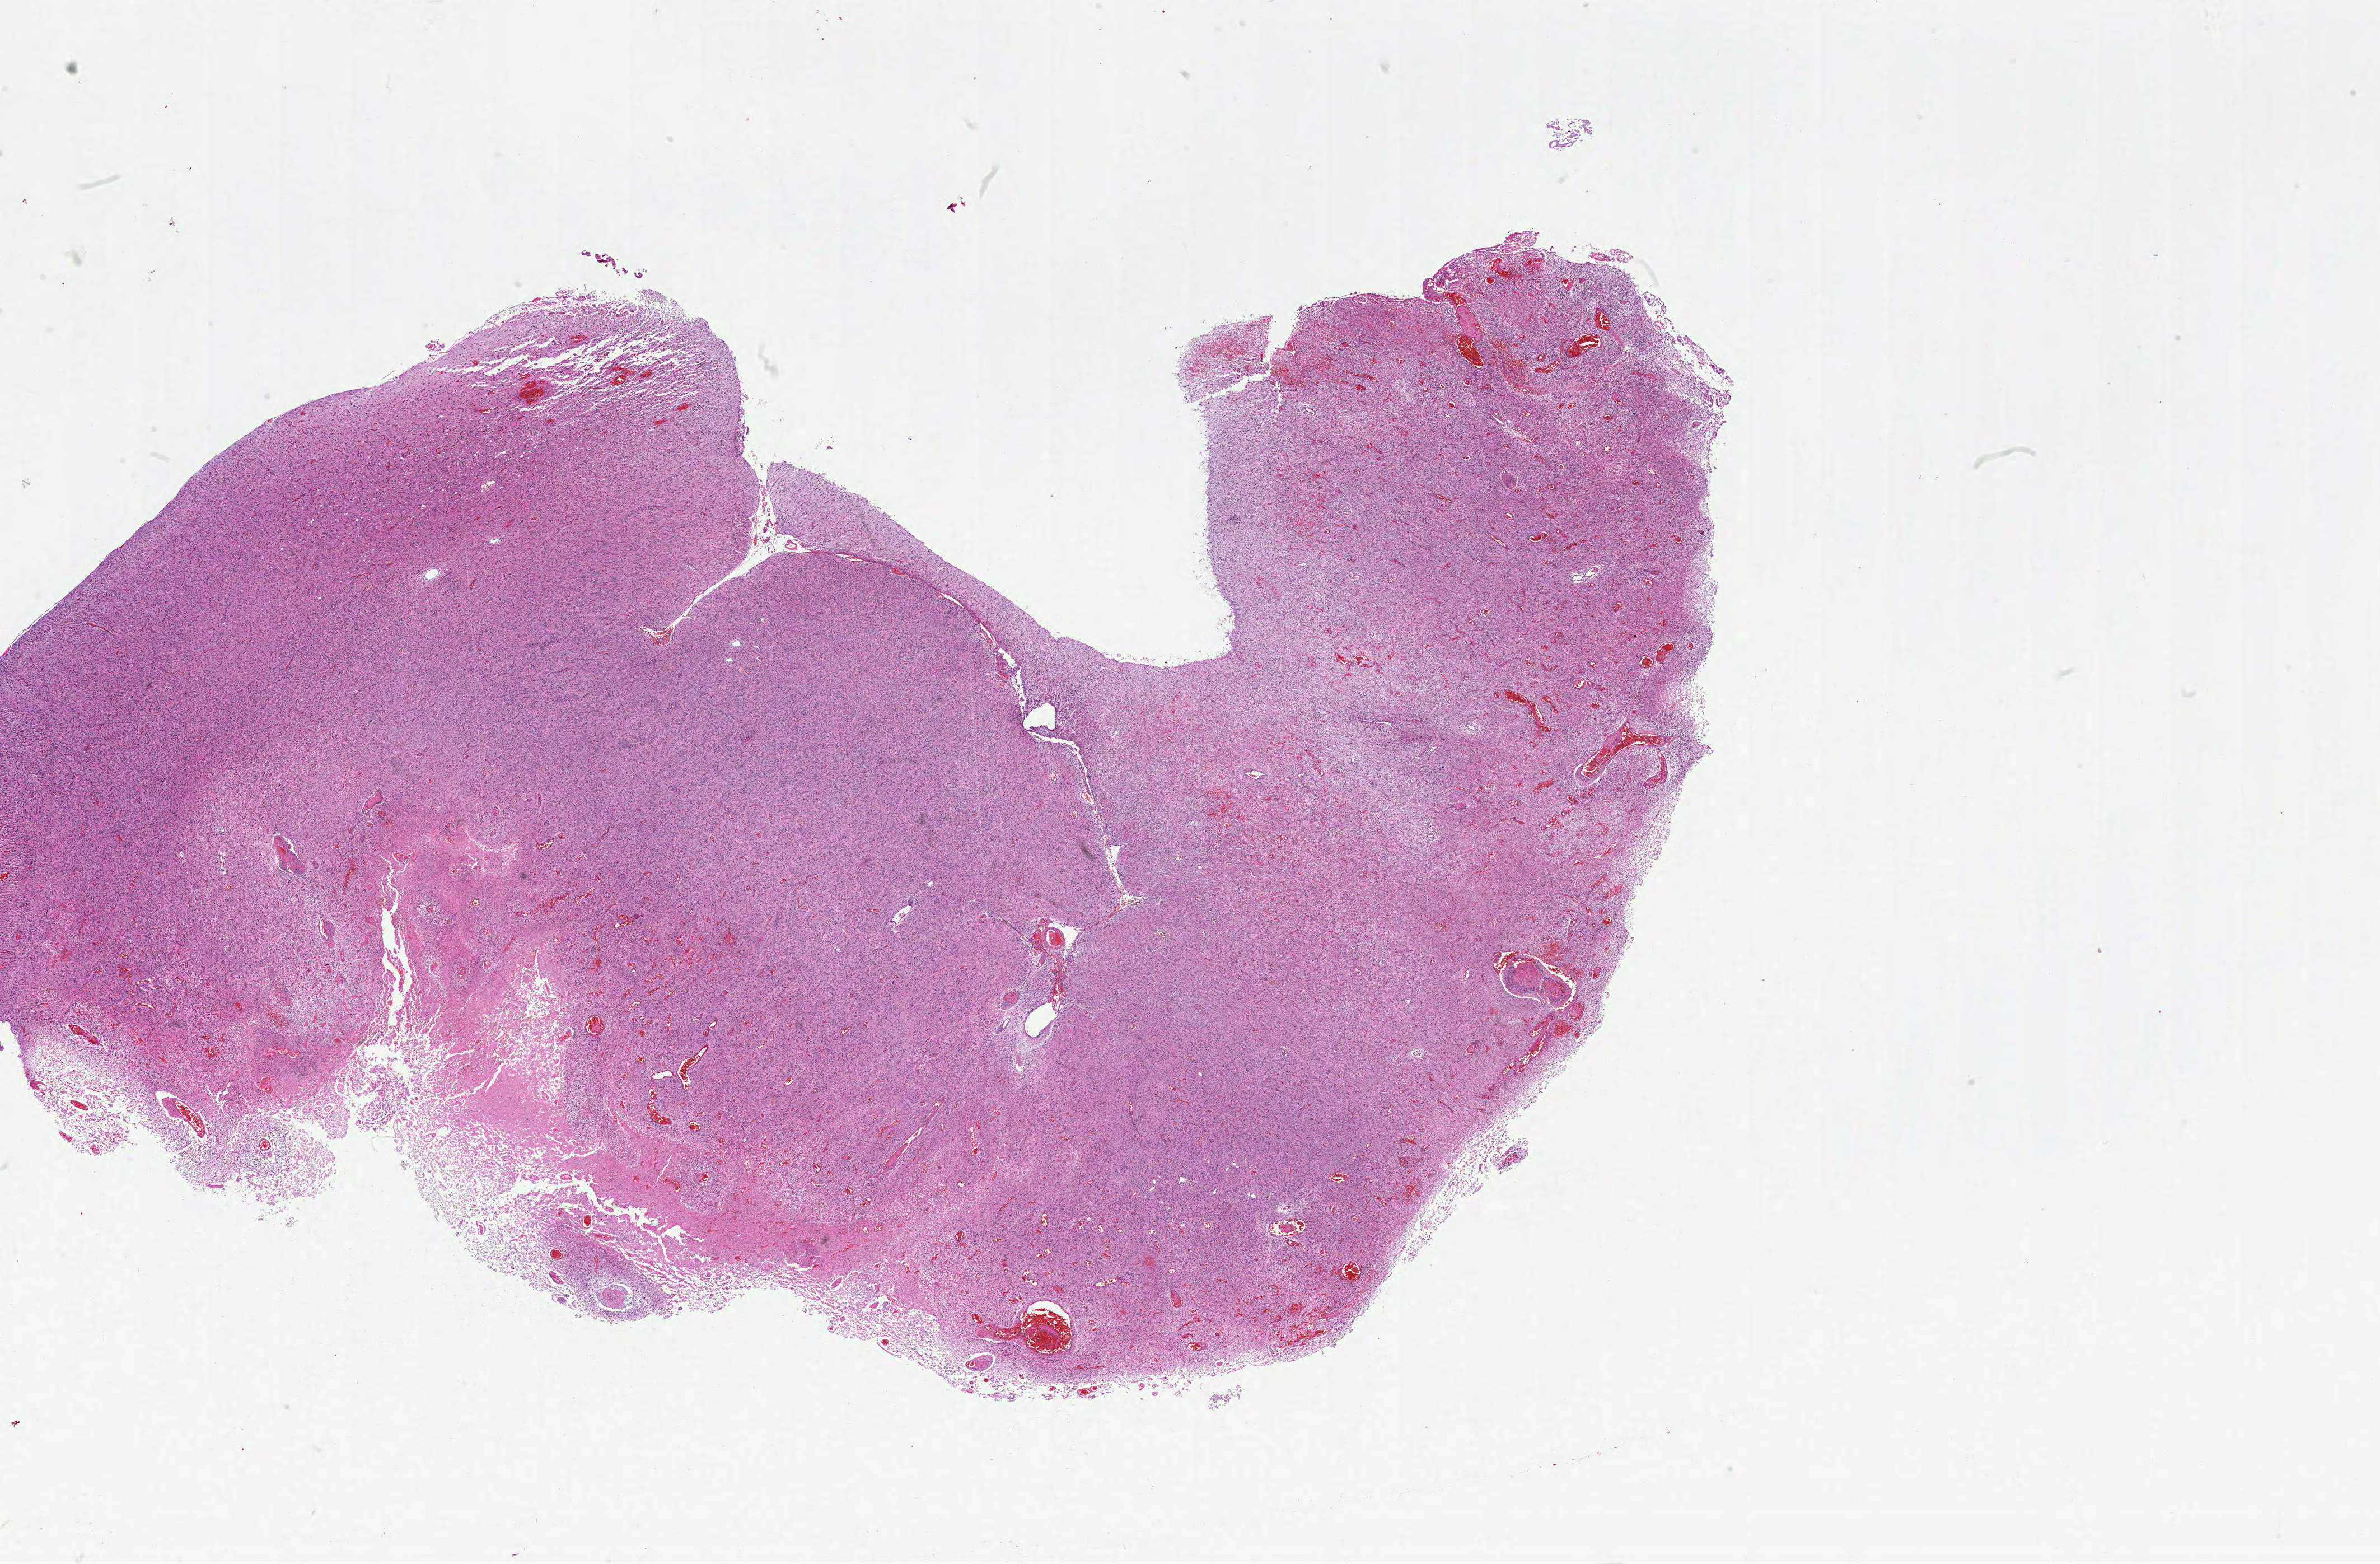
Whole-slide histology image, Hematoxylin and eosin (H&E) stained — low-resolution overview of the scanned area, about 34.0 x 22.3 mm (from a 20x scan); FFPE section; sample: primary tumour, brain. Male patient; age at initial diagnosis 55 years.
Pathologic diagnosis: Glioblastoma.